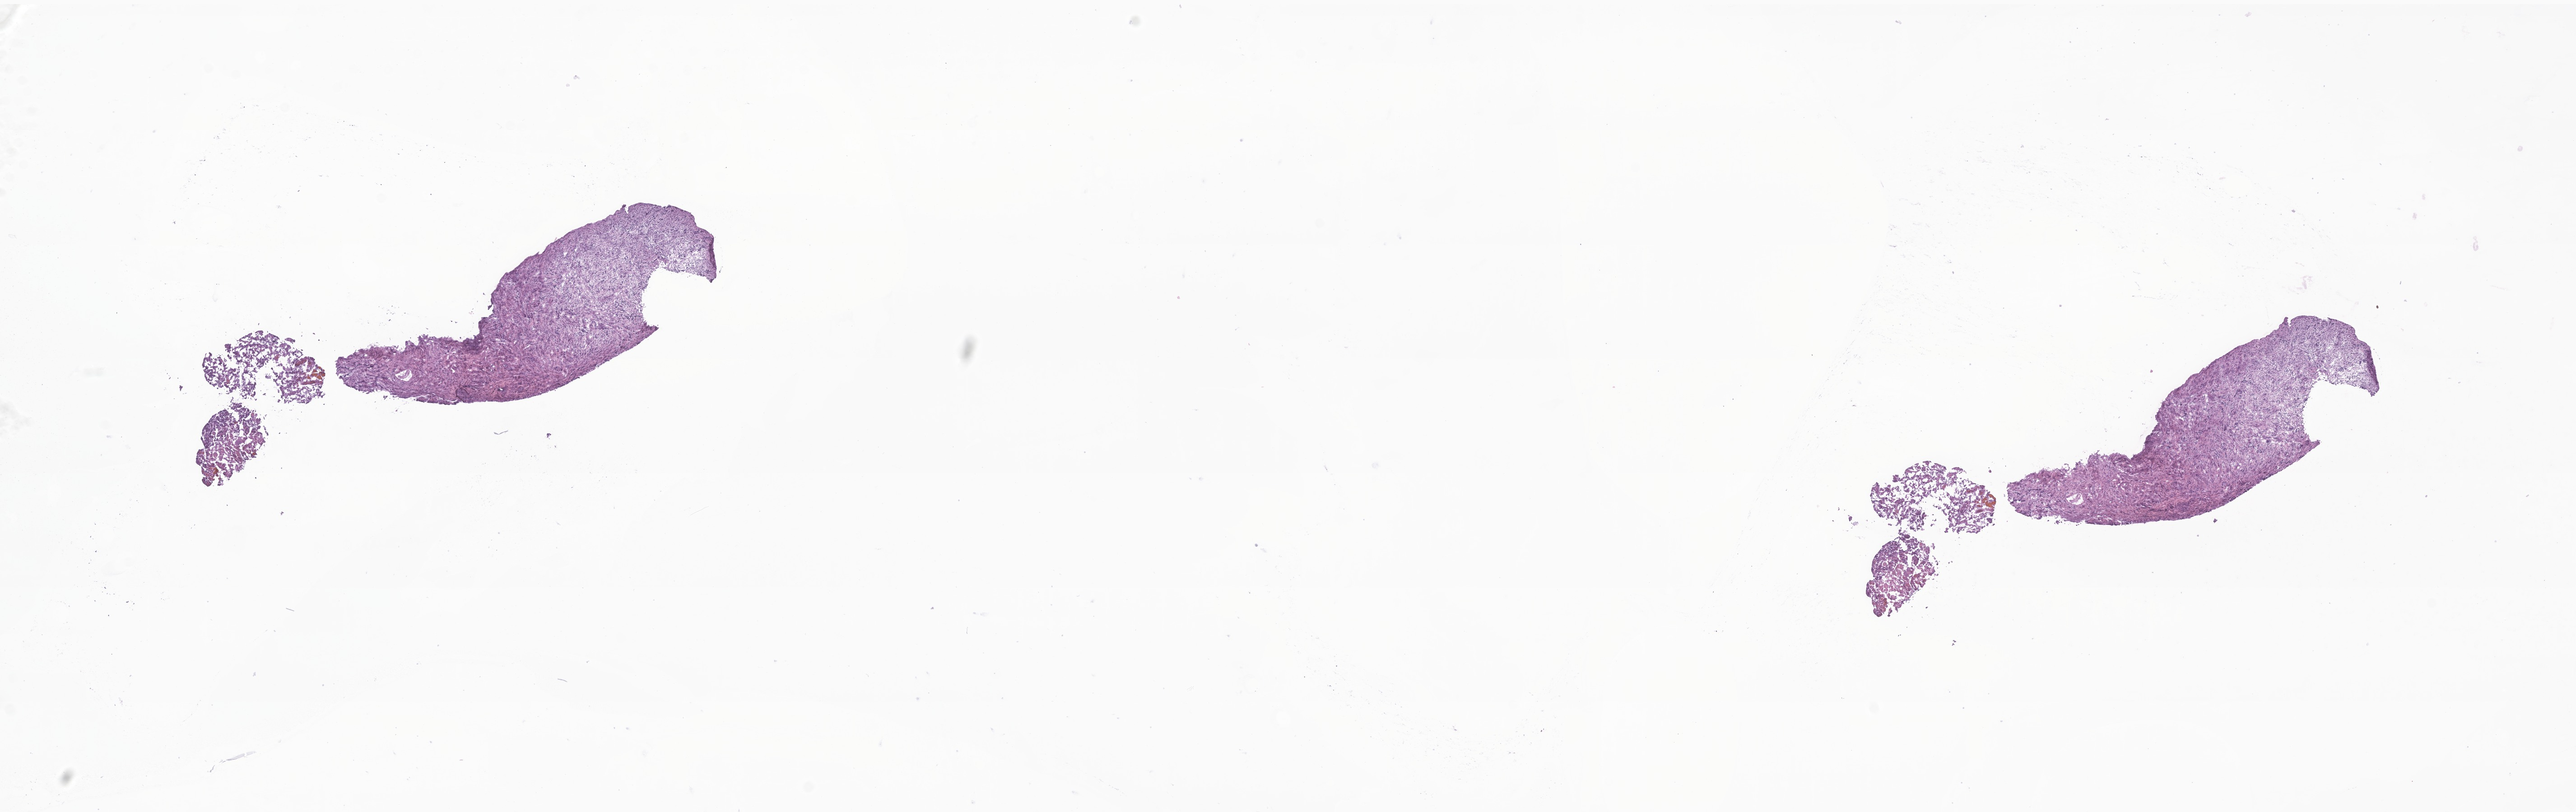
Whole-slide image, hematoxylin and eosin (H&E) stain of tumor tissue from the brain, a low-resolution overview of the entire scanned area, about 24.1 x 7.6 mm. Cryosection (OCT / tissue freezing medium). Male patient, age 199 months (16 years 7 months).
Diagnosis (ICD-O-3 morphology term): Medulloblastoma, NOS.